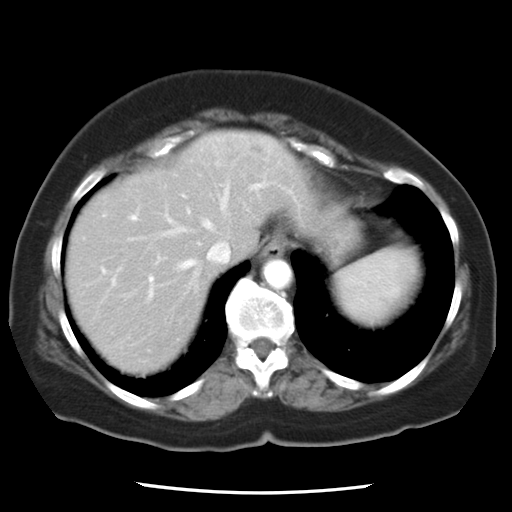
Contrast-enhanced abdominal CT, one axial slice. Slice 20 of 24 in the series (ordered by position). Reconstruction kernel STANDARD. 120 kVp. Soft-tissue window (W 400 / L 40 HU). 512 × 512 image matrix. Female patient, age 71 years. From the clinical record (not read from this slice): diagnosis: colorectal cancer liver metastases, imaged before liver resection; multiple liver metastases: no; largest metastasis: 4.3 cm.
Outlined on this slice (outlined manually by an expert reader):
- hepatic veins: bounding box (x1, y1, x2, y2) in pixels: (135, 185, 231, 300)
- liver: (67, 131, 304, 373)
- planned liver remnant (the part of the liver to remain after resection): (67, 154, 253, 373)
- portal vein (with intrahepatic branches): (131, 147, 296, 281)
- liver metastasis: (247, 143, 268, 159)